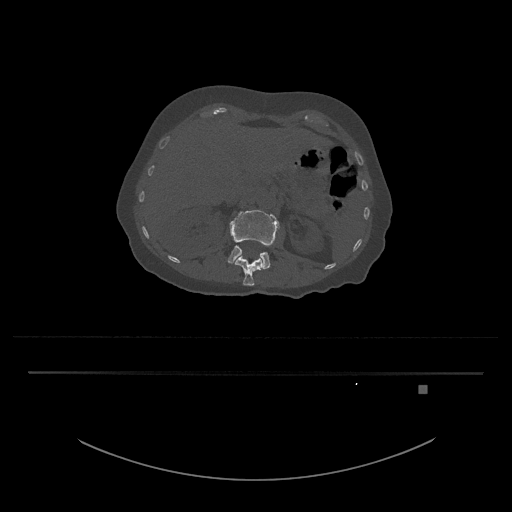
CT including the spine, one axial slice; slice 522 of 797 in the series (ordered by position); reconstruction kernel Br40s/3; 120 kVp; bone window (W 1800 / L 400 HU); 0.5 mm slice thickness; 512 × 512 image matrix, field of view 500 × 500 mm. Female patient, age 57 years. From the clinical record (not read from this slice): primary cancer: cervical.
Structures marked on this image (semi-automatically segmented with operator editing):
- L1 vertebra: bounding box [x1, y1, x2, y2] px = [235, 255, 263, 286]